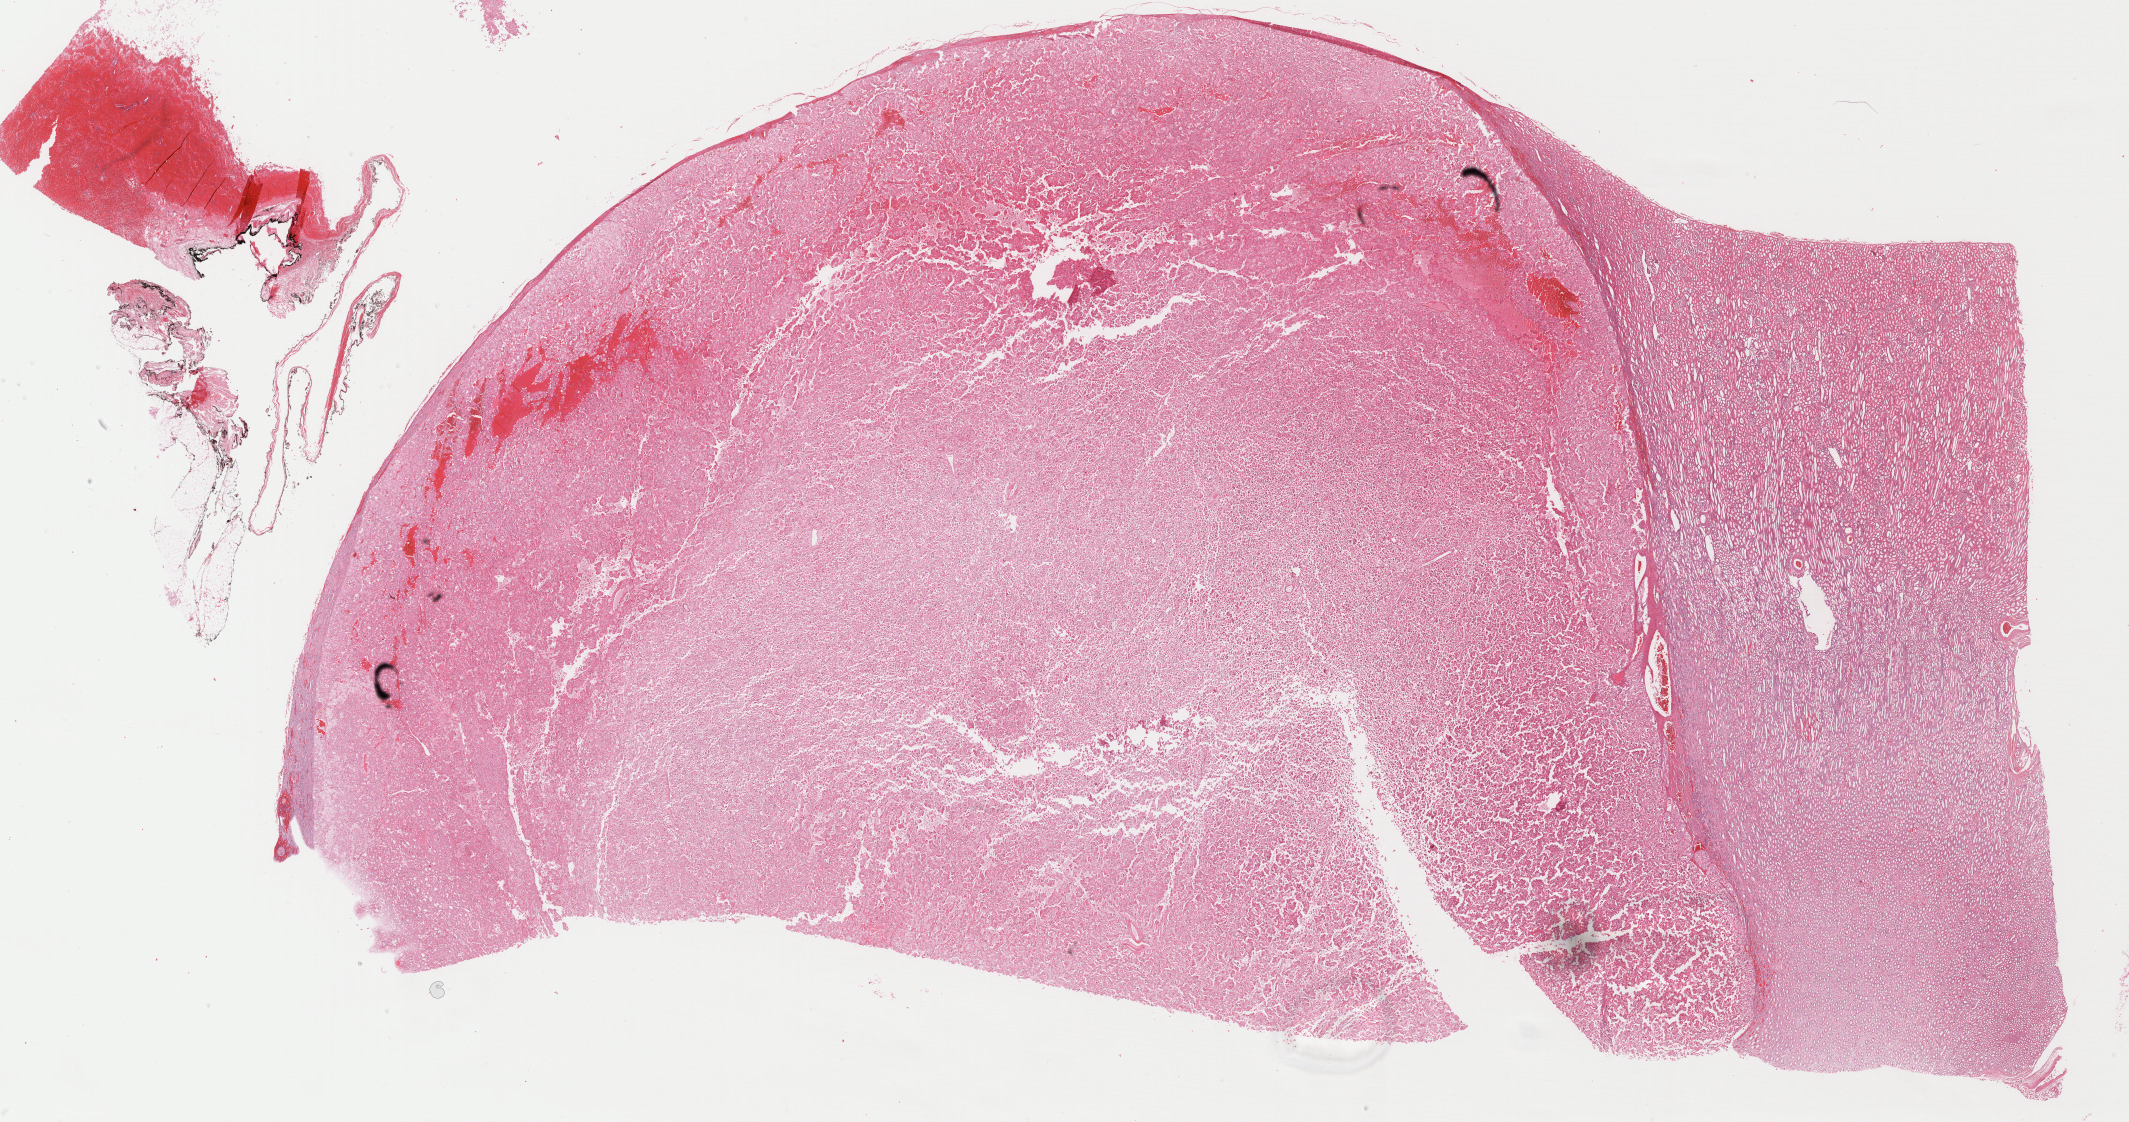
Digitized H&E tissue section (whole slide), whole scanned area (about 34.3 x 18.1 mm) shown as a low-resolution overview, FFPE section, sample: primary tumour, kidney. Patient: female, age at initial diagnosis 28 years.
- AJCC pathologic stage: I (6th edition)
- pathologic diagnosis: Renal cell carcinoma, chromophobe type
- TNM: T1a N0
- laterality: right